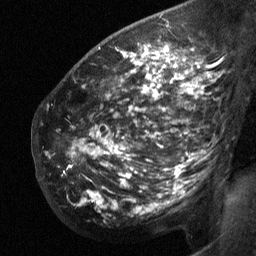
Breast MRI (dynamic contrast-enhanced), one sagittal slice; position 41 of 64 along the scan axis; dynamic contrast-enhanced study with each time point stored as its own series, time point 2 of 3 at this slice position (early post-contrast, ordered by acquisition time); 1.5 T; TE 4.8 ms, TR 27 ms; 256 × 256 image matrix, field of view 200 × 200 mm. Female patient, age 50 years. Case-level facts recorded for this patient, not image findings: setting: breast cancer imaged before/during neoadjuvant chemotherapy; receptor status: HER2-positive.
Structures marked on this image (semi-automatic segmentation, software-assisted and operator-edited):
- analysis volume of interest (the breast-tissue region the enhancement analysis was run in; not a lesion): box from (x=50, y=62) to (x=209, y=199) px
- tumour enhancement mask (voxels above the 90 % enhancement threshold inside the analysis volume of interest): (x=136, y=62)–(x=190, y=90)